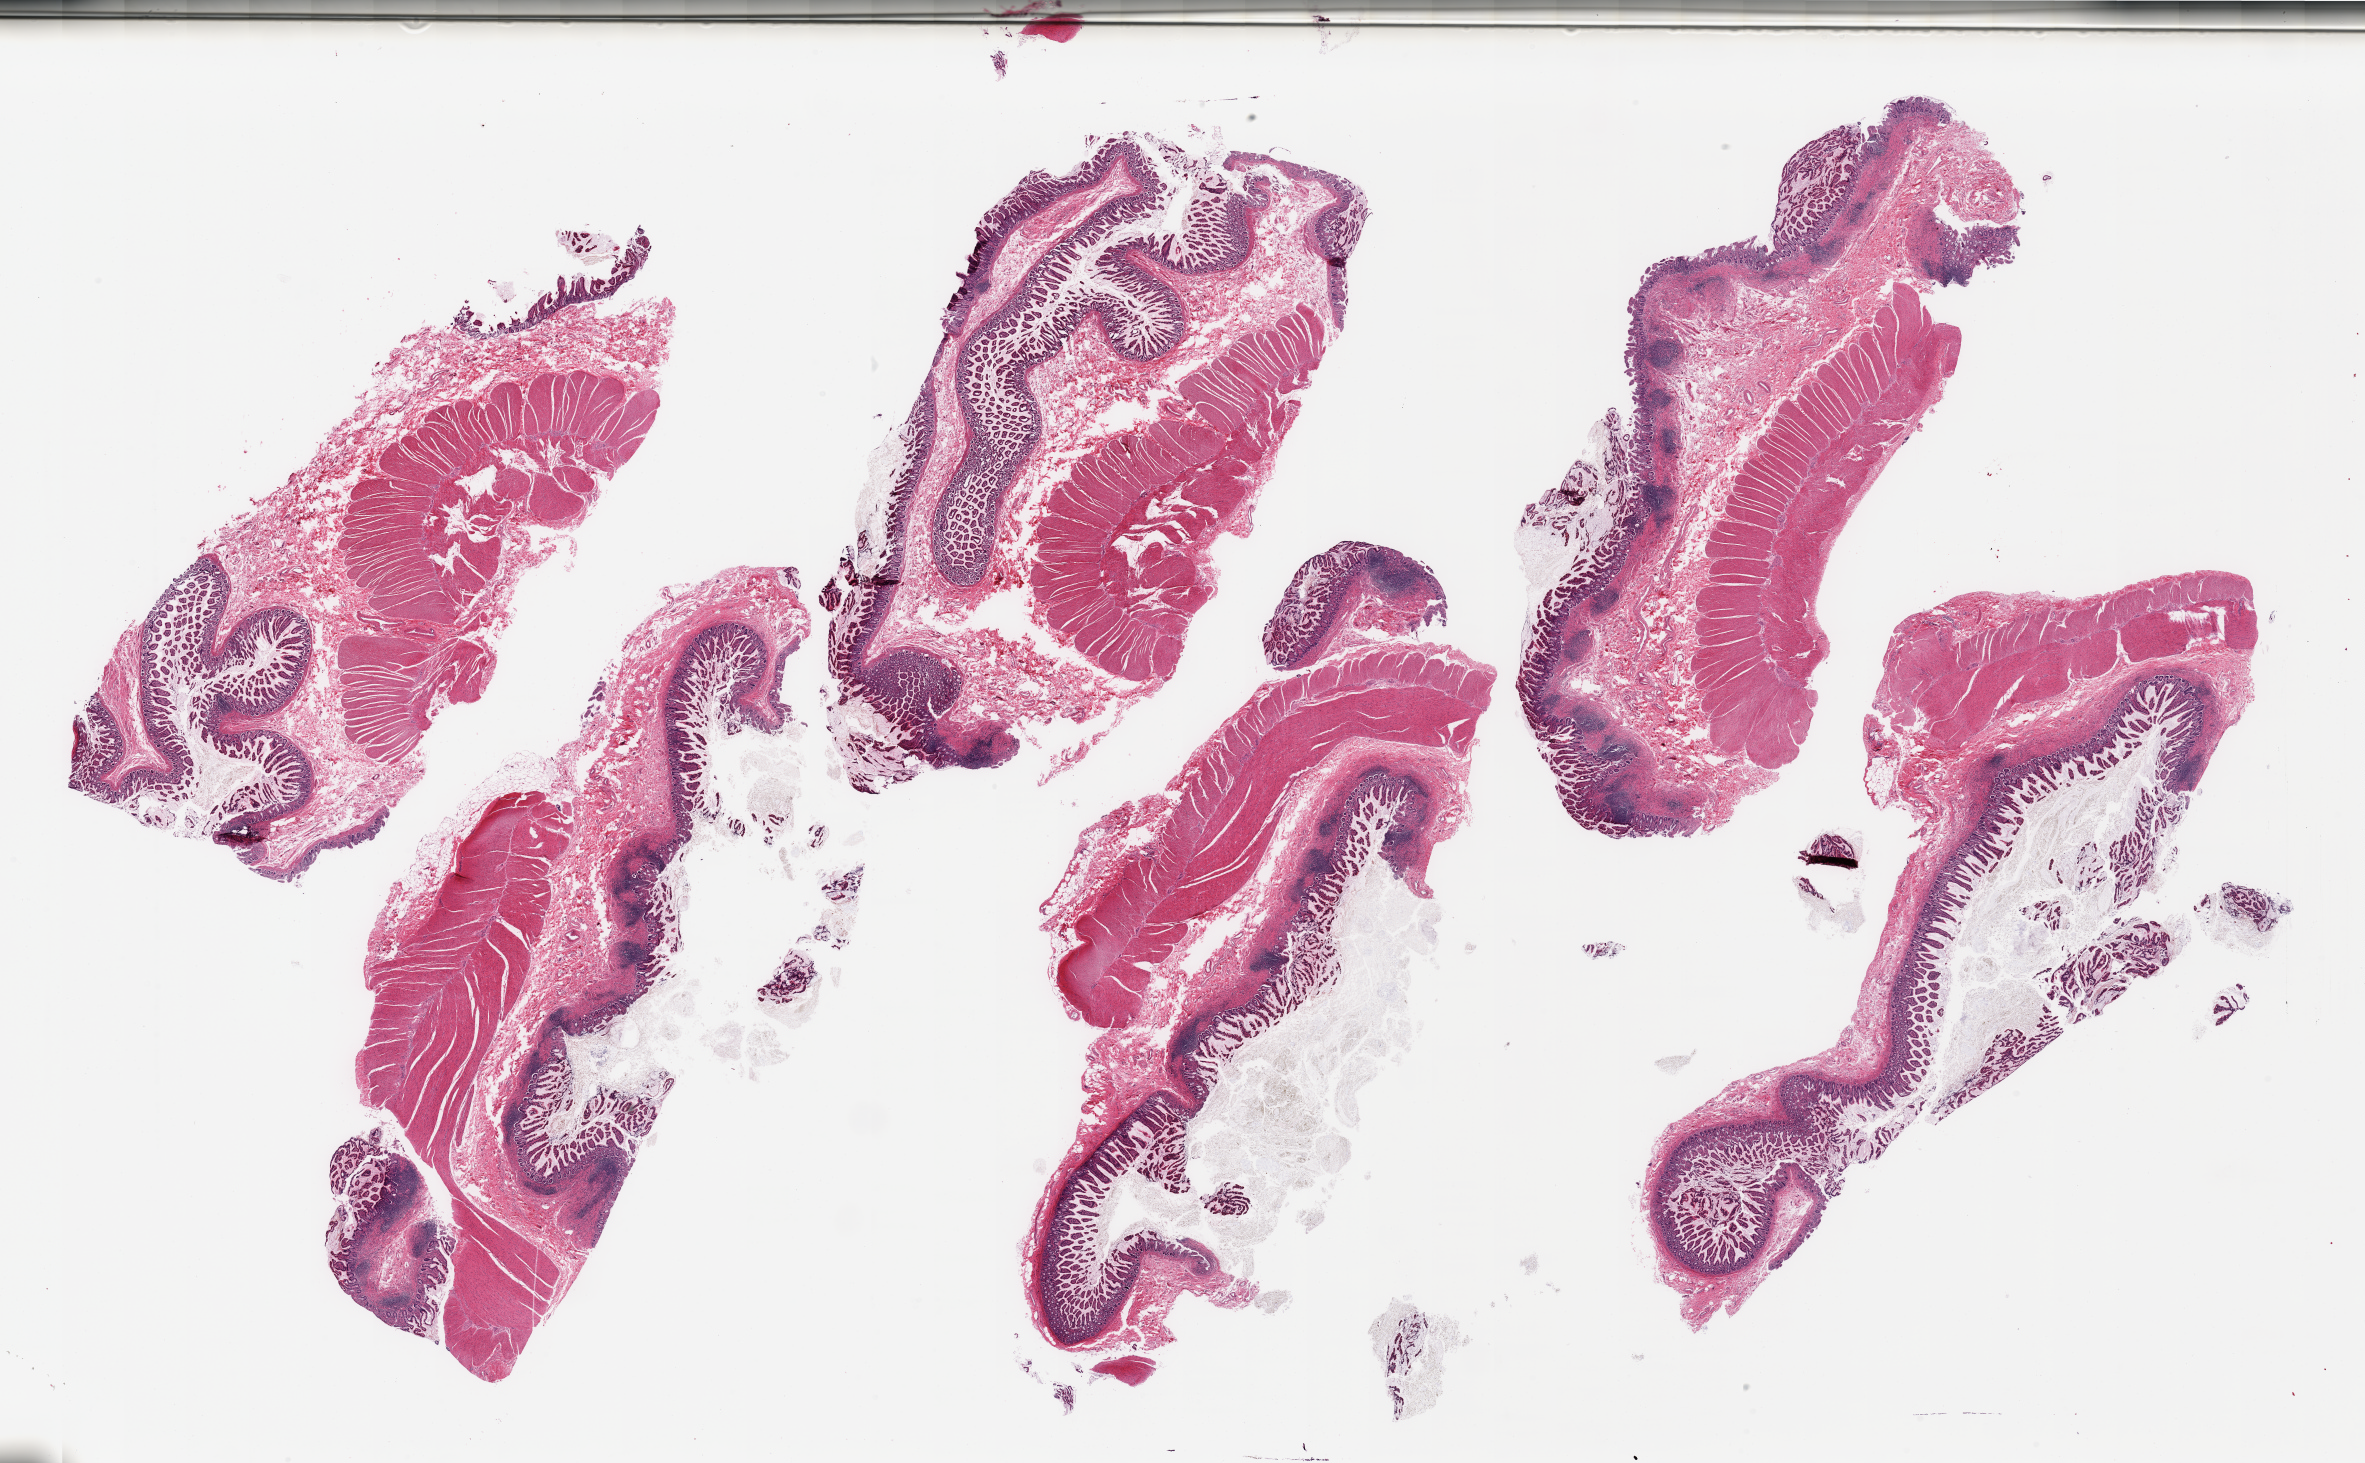
Whole-slide image, hematoxylin and eosin (H&E) stain, a low-resolution overview of the entire scanned area, about 37.4 x 23.1 mm, PAXgene-fixed, paraffin-embedded tissue, target tissue: ileum, tissue donor sample. Donor: female.
Pathologist's review note for this sample: 6 pieces, target lymphoid aggregates present; sample carefully, < 10% tissue.